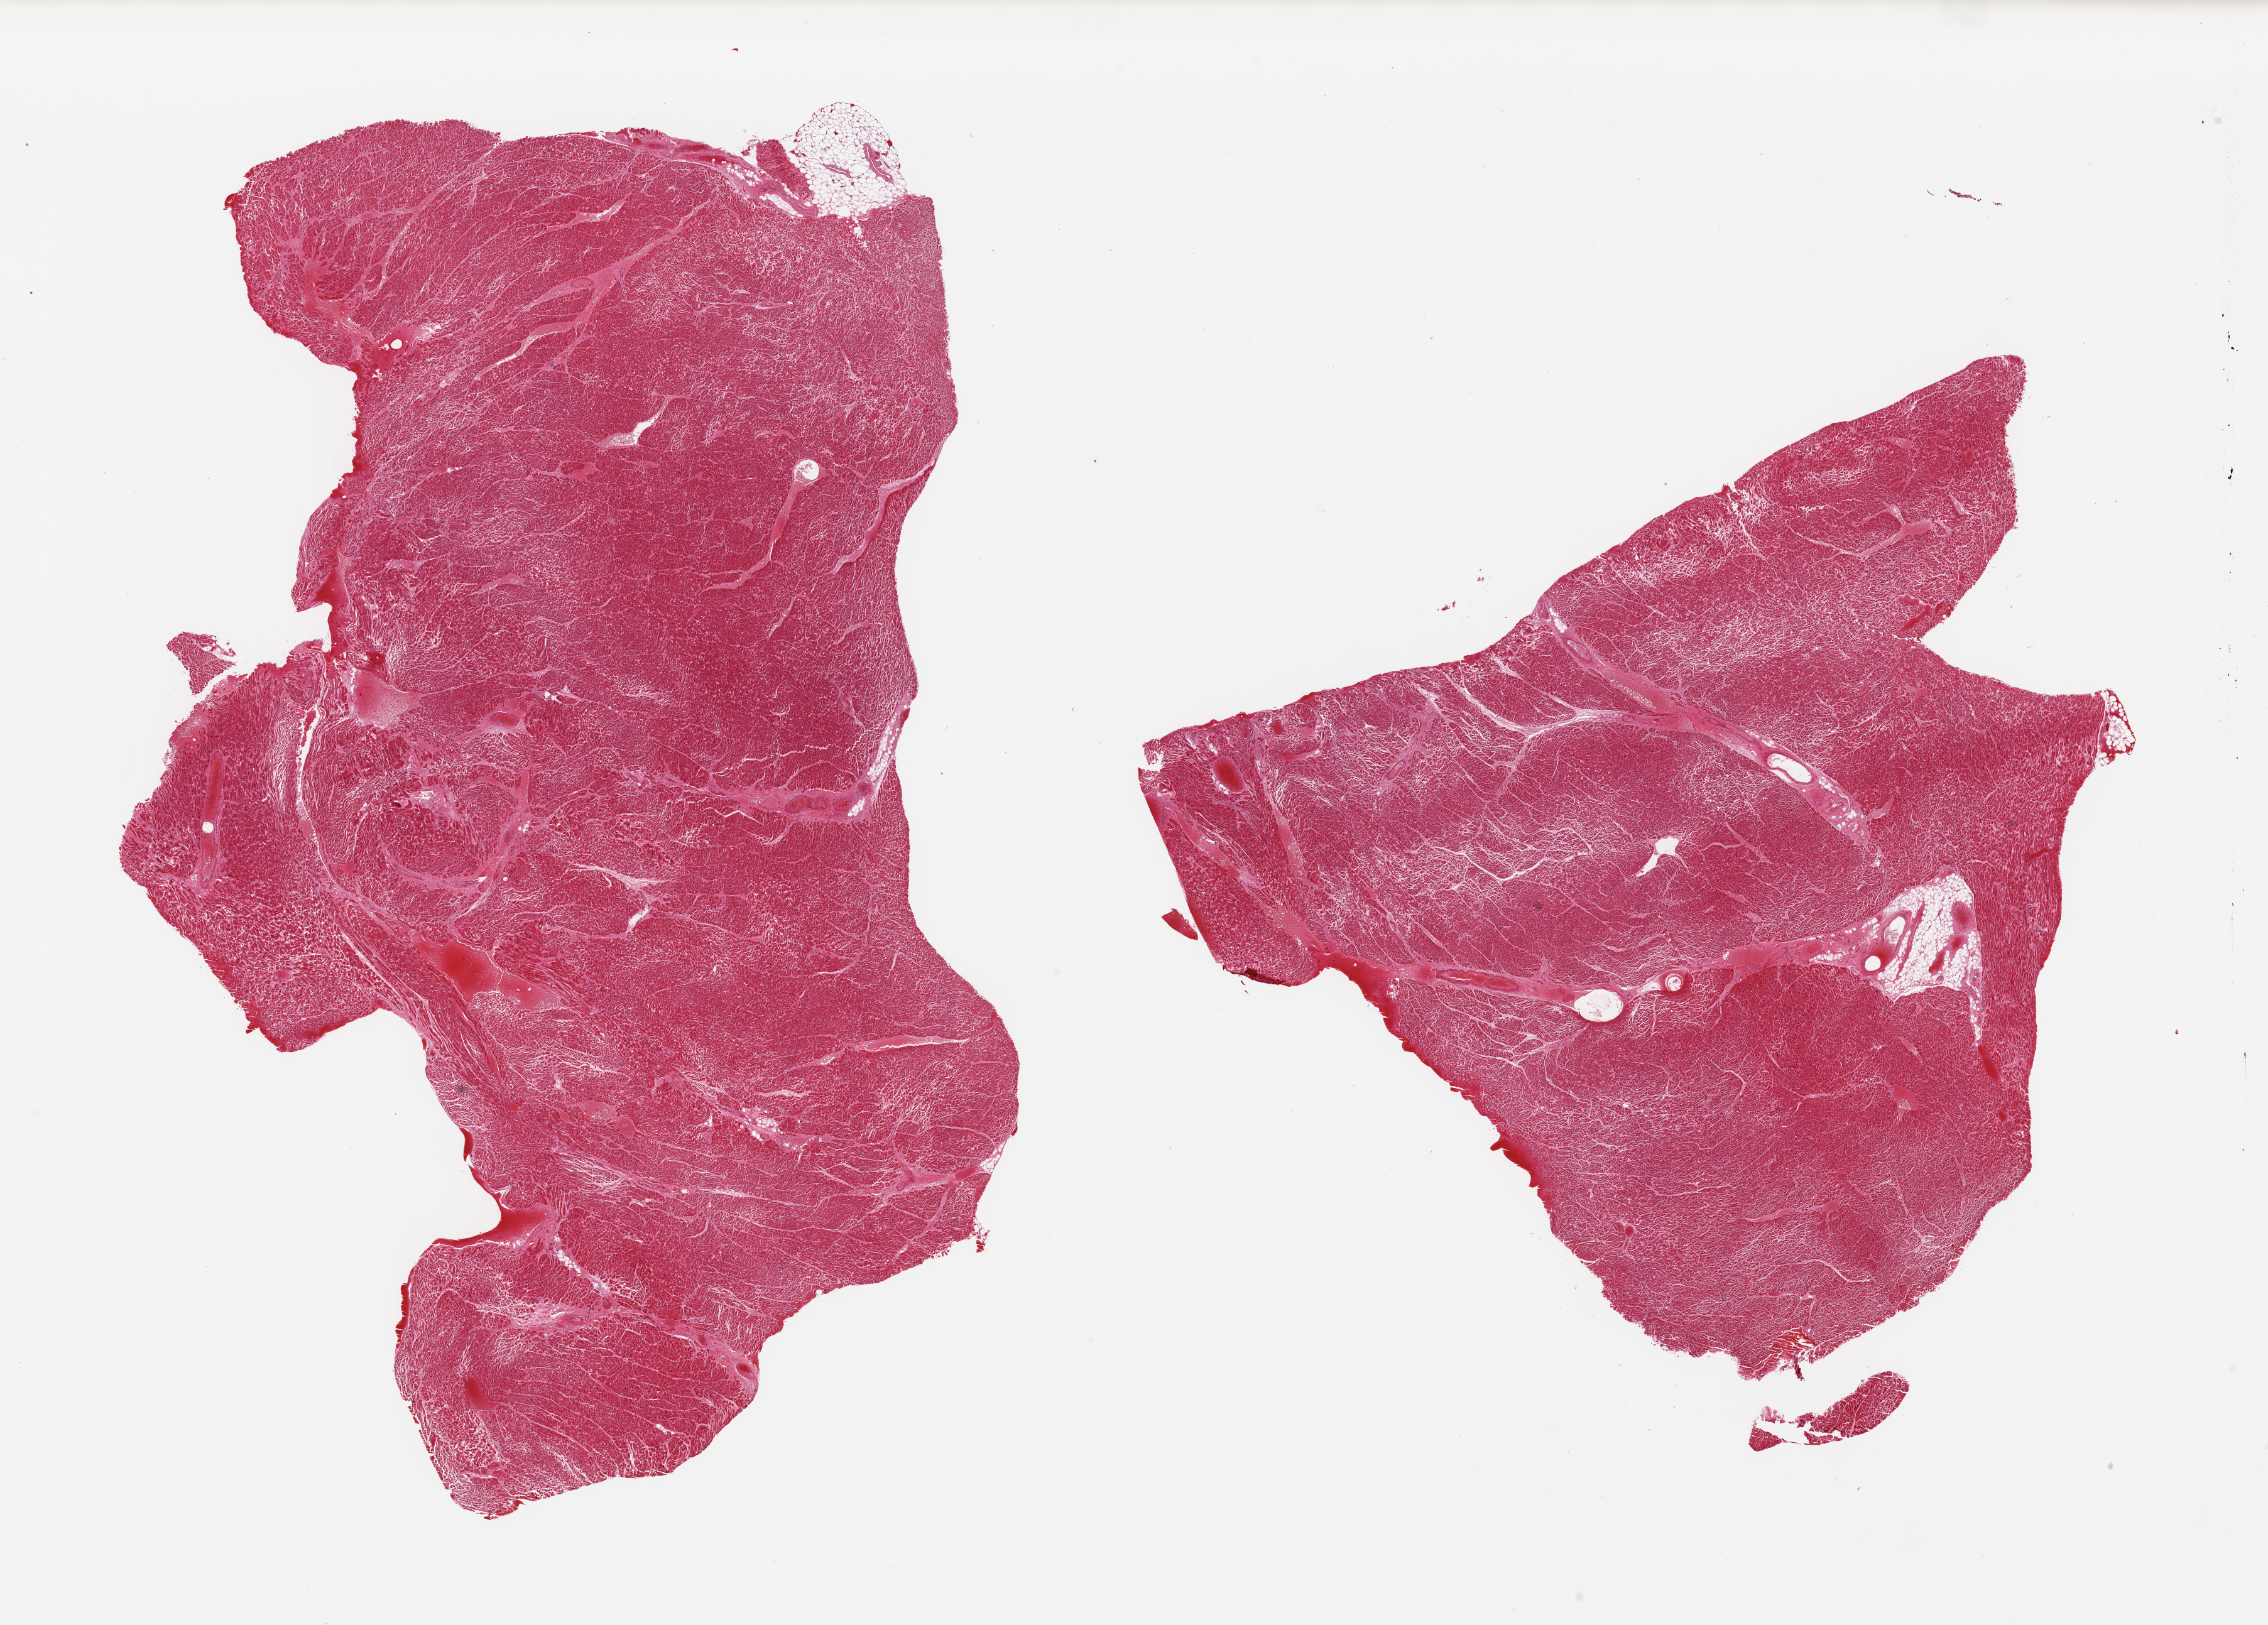
Whole-slide image, hematoxylin and eosin (H&E) stain — whole scanned area (about 28.5 x 20.5 mm, from a 20x scan) shown as a low-resolution overview. PAXgene-fixed paraffin-embedded (PFPE) section. Section of heart (target tissue). Donor tissue sample. Donor: female.
Pathologist's review note for this sample: 2 pieces, mild chronic ischemic changes.